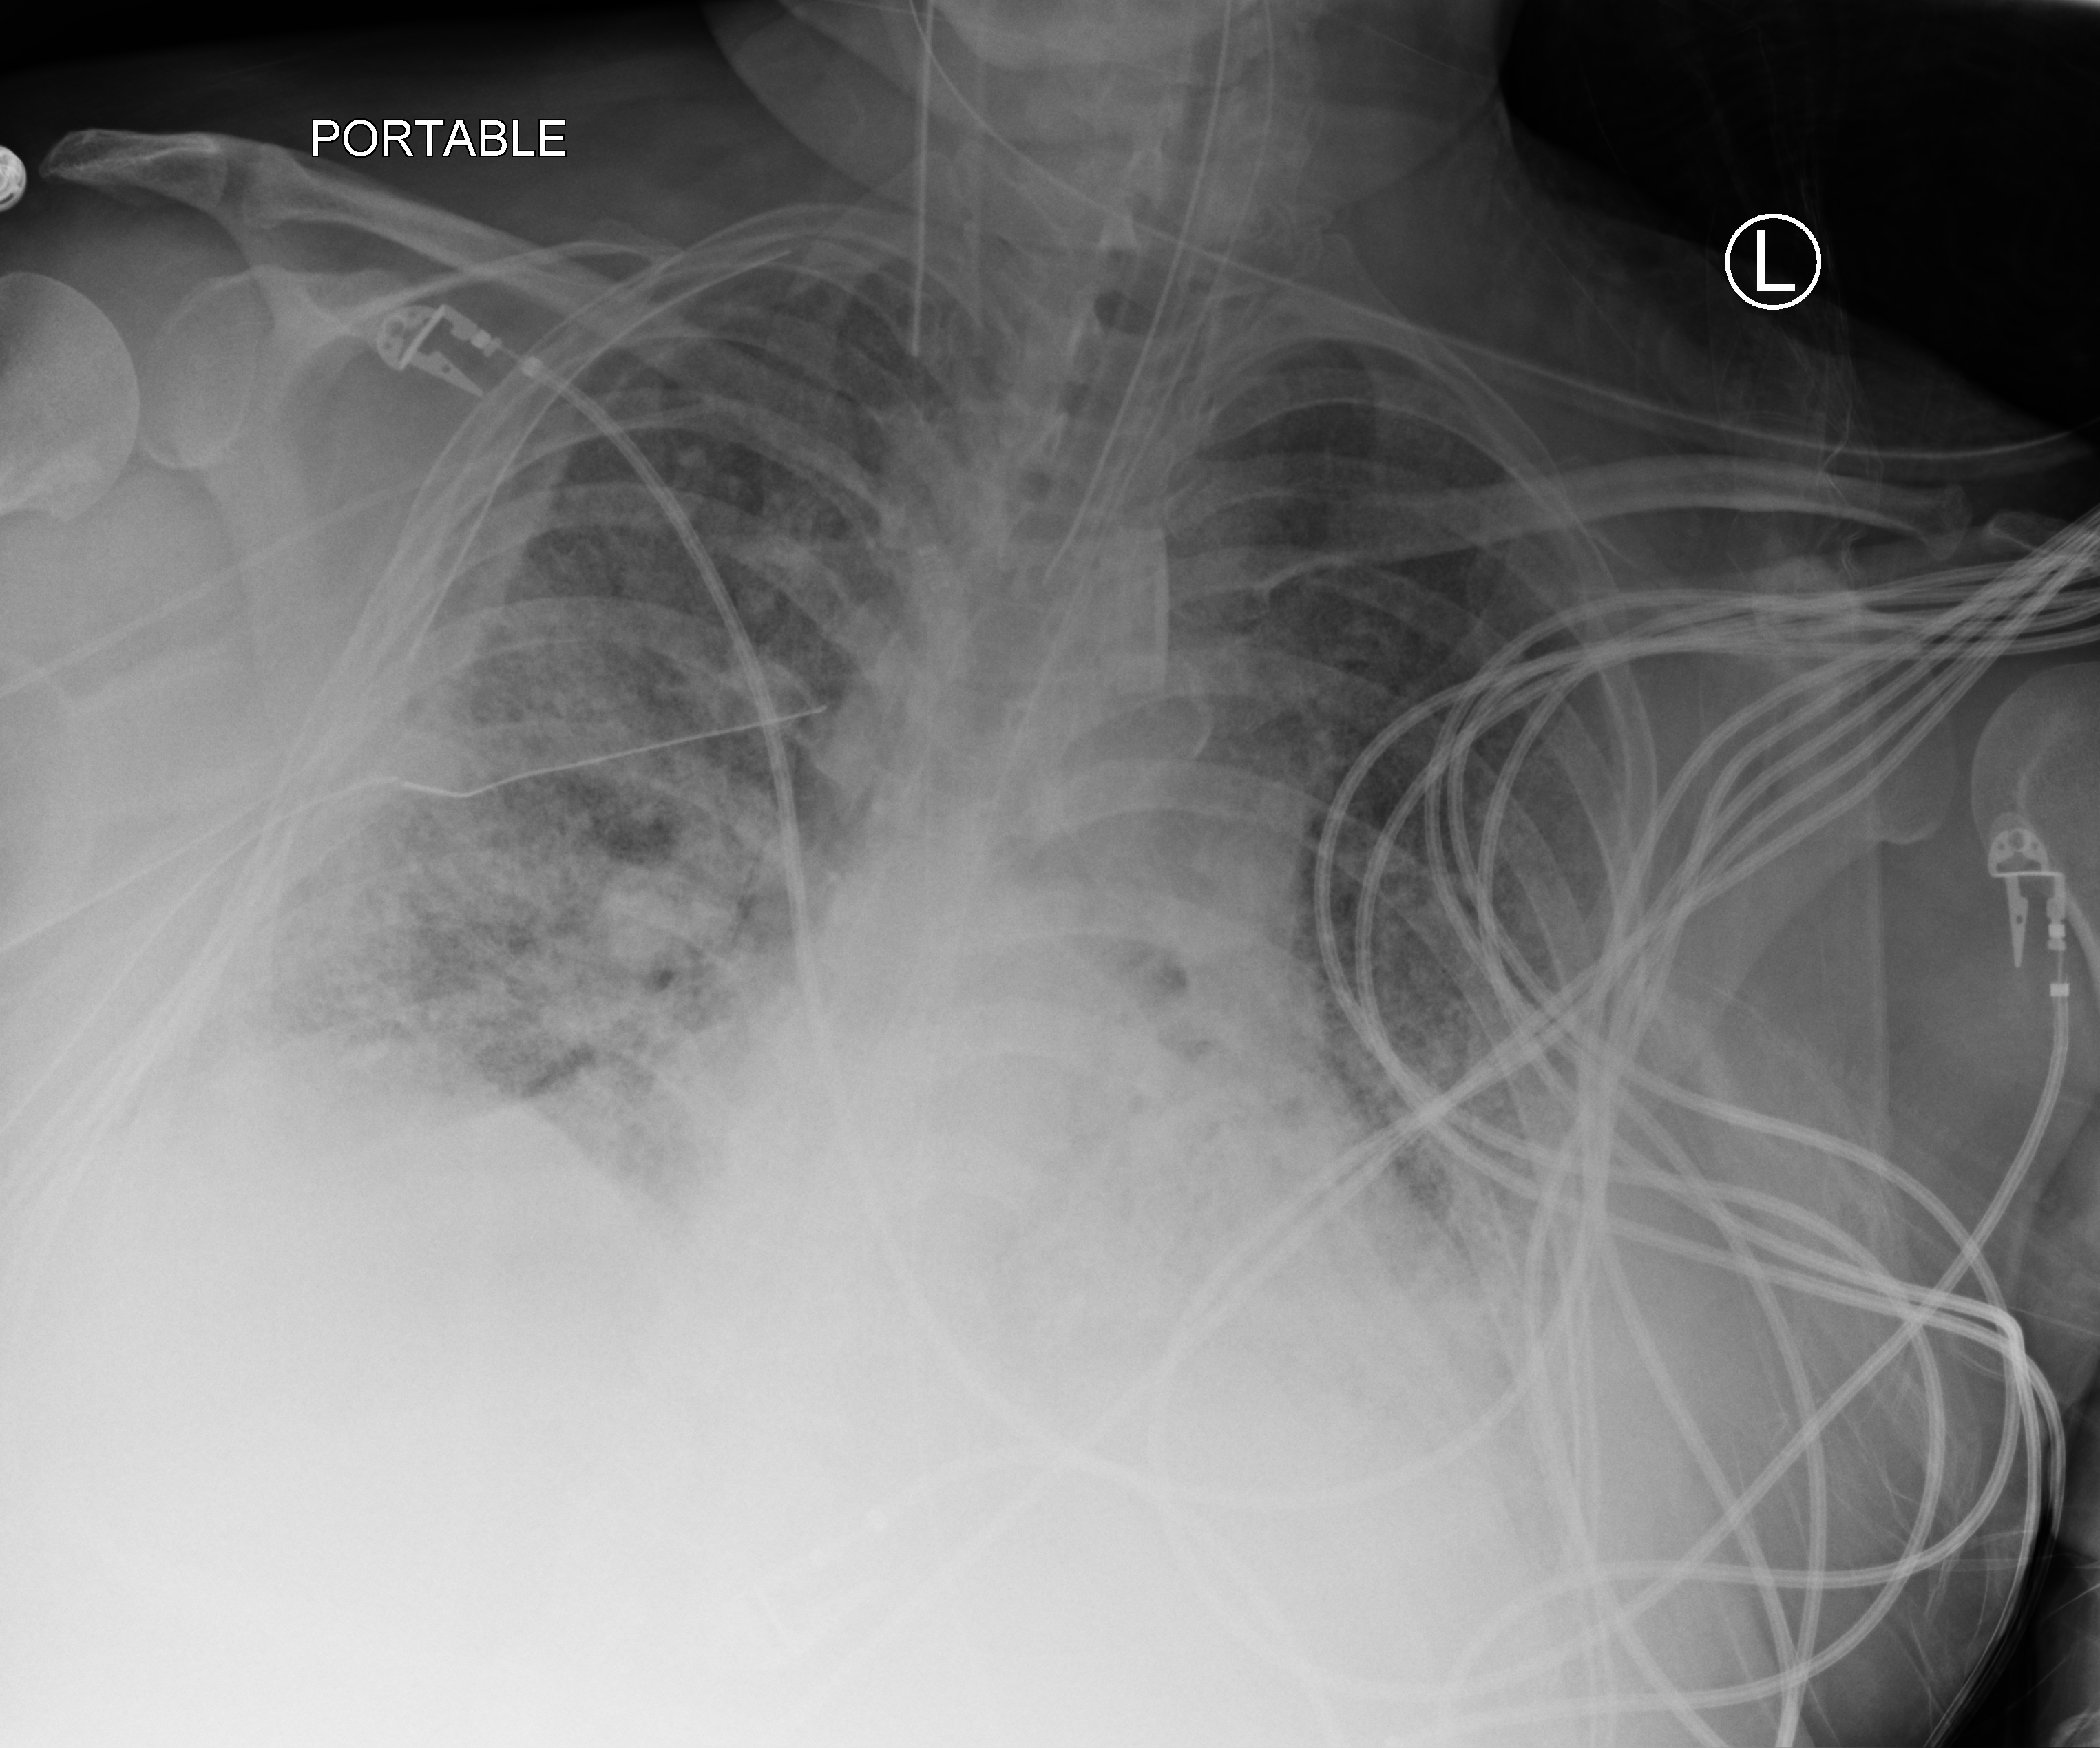
Chest X-ray (portable). Patient hospitalised with COVID-19, aged 18–59 years.
Admission-level facts for this patient (not findings on this image; timing relative to this image not recorded): smoking status (admission record): never; hypertension (admission record): no; mechanically ventilated during this hospital stay: yes.